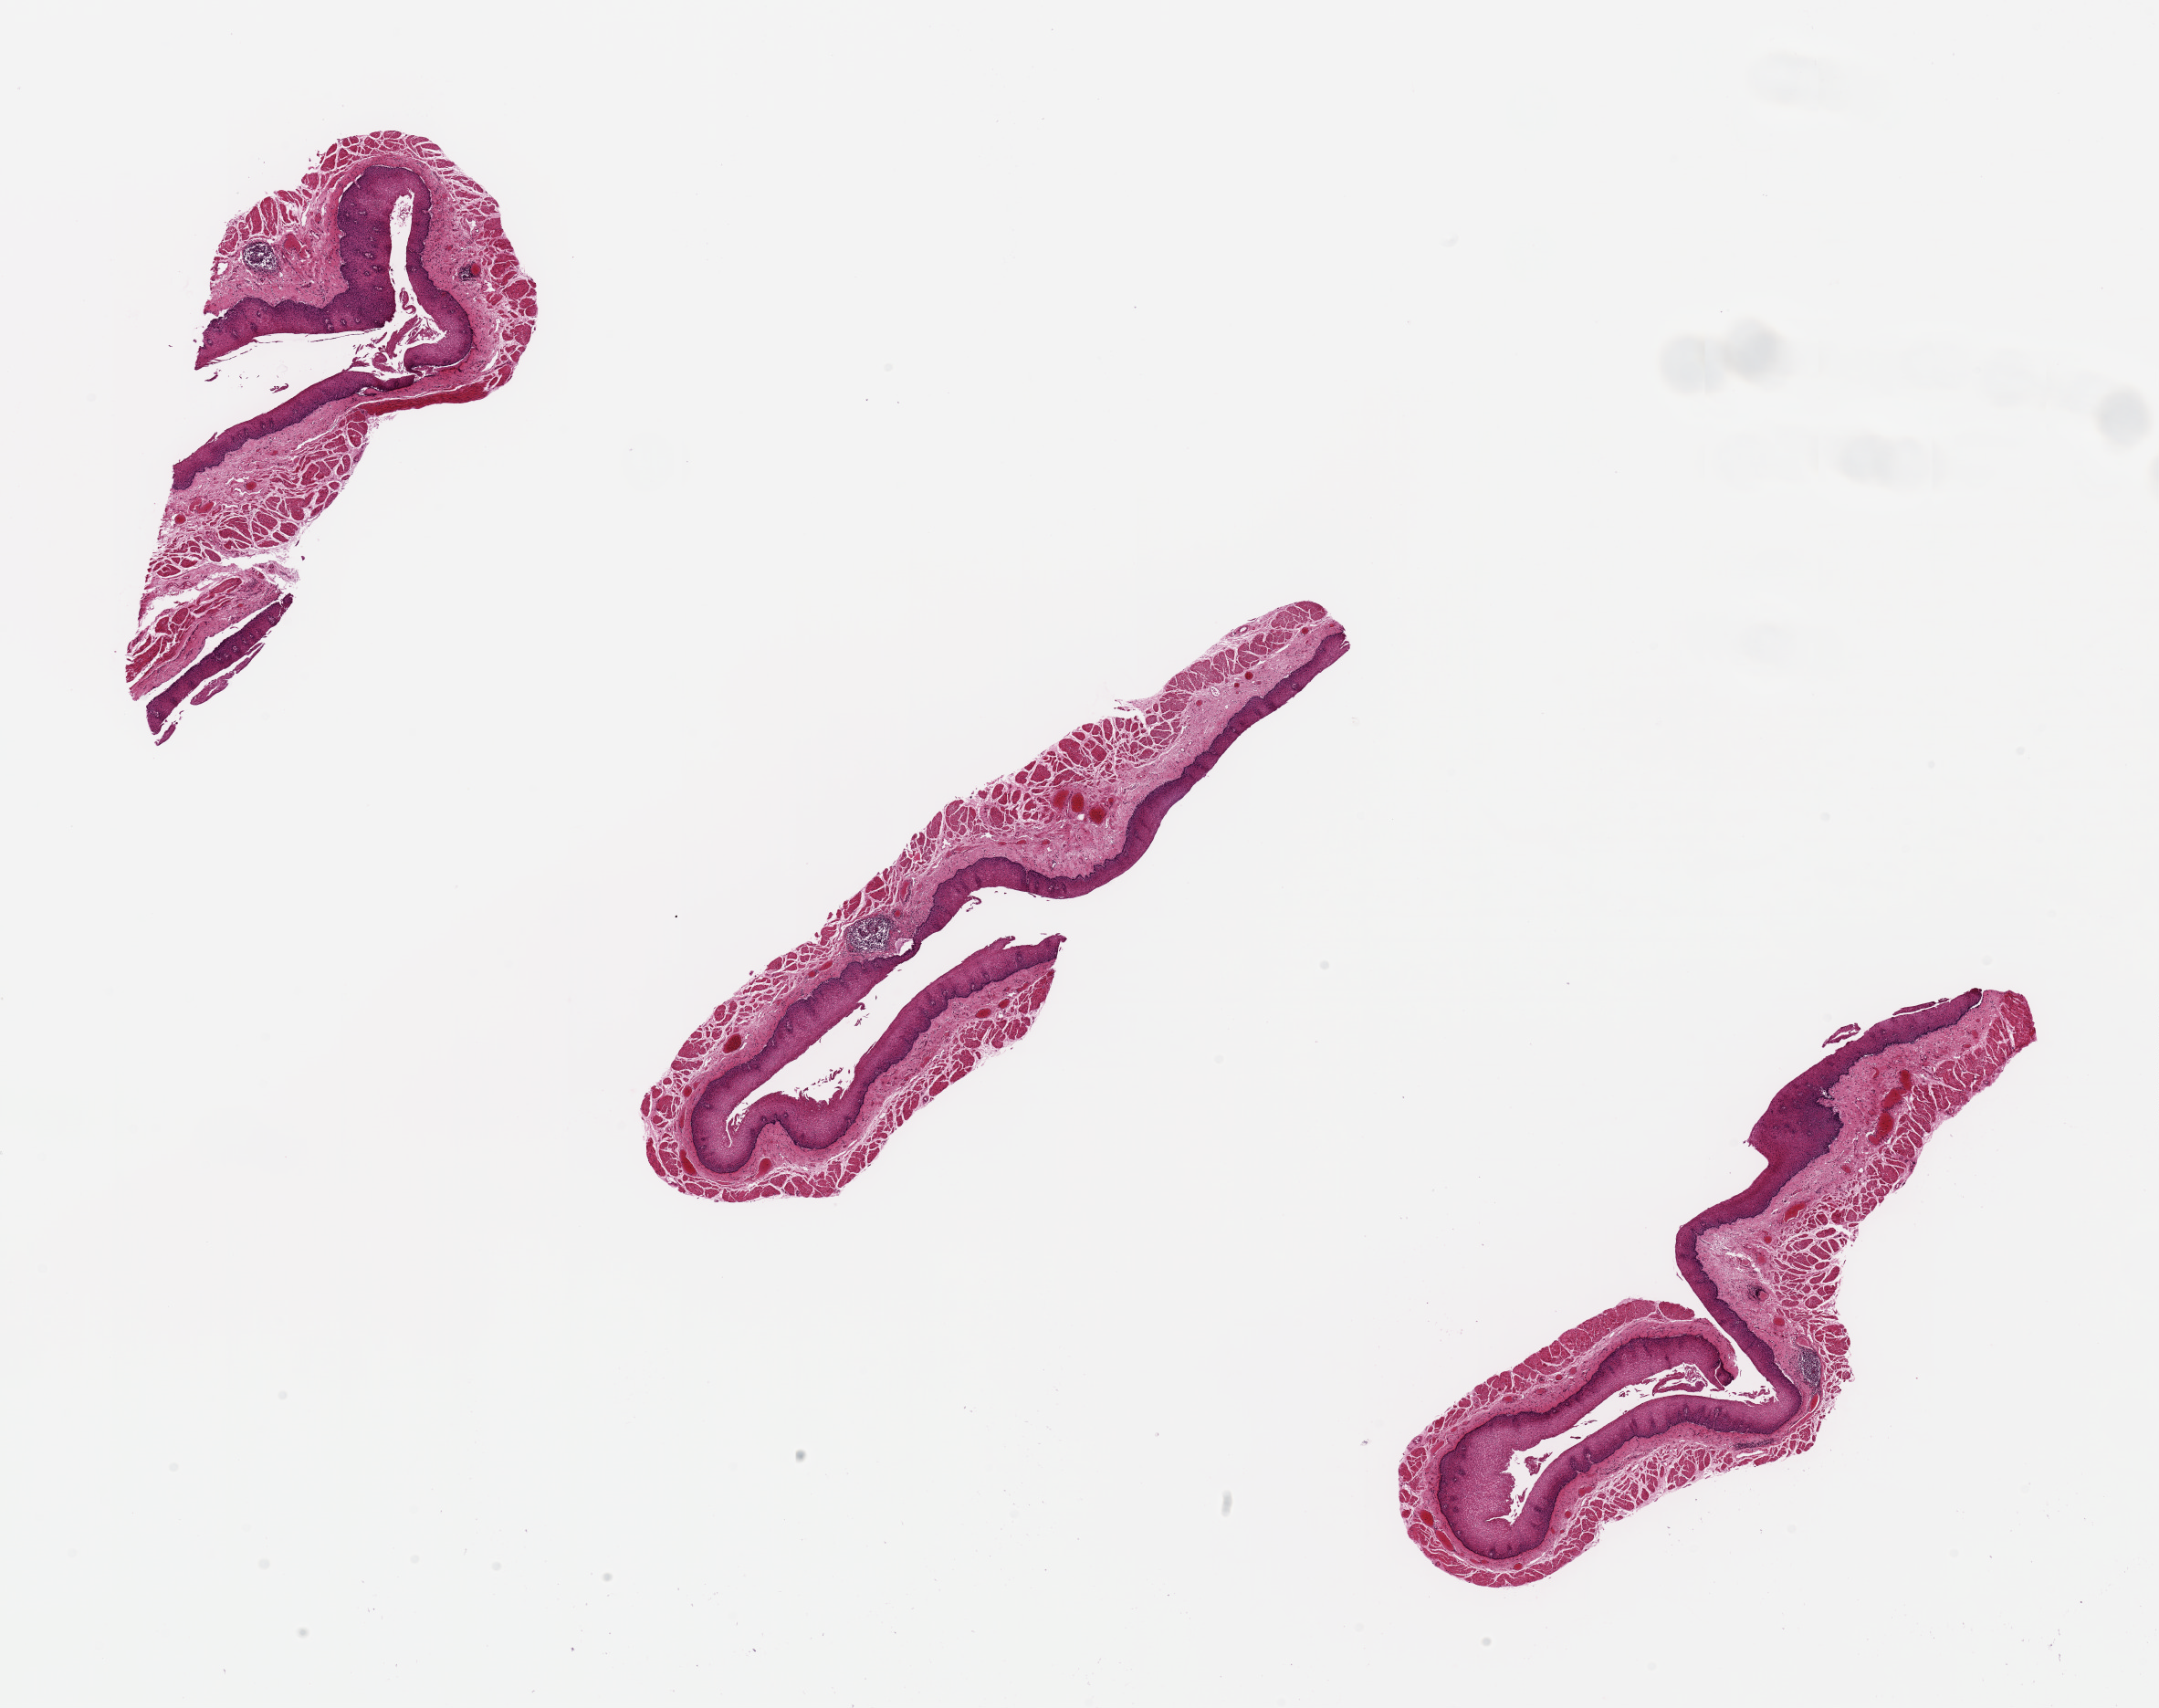
Whole-slide image, hematoxylin and eosin (H&E) stain — low-resolution overview of the scanned area, about 18.7 x 14.8 mm (acquisition: 20x scan). PAXgene-fixed, paraffin-embedded tissue. Sampled site (target tissue): esophageal mucous membrane. Donor tissue sample. Female donor.
• reviewer comment on this tissue sample: 3 10x1mm pieces. Mucosa is ~10% of specimen thickness